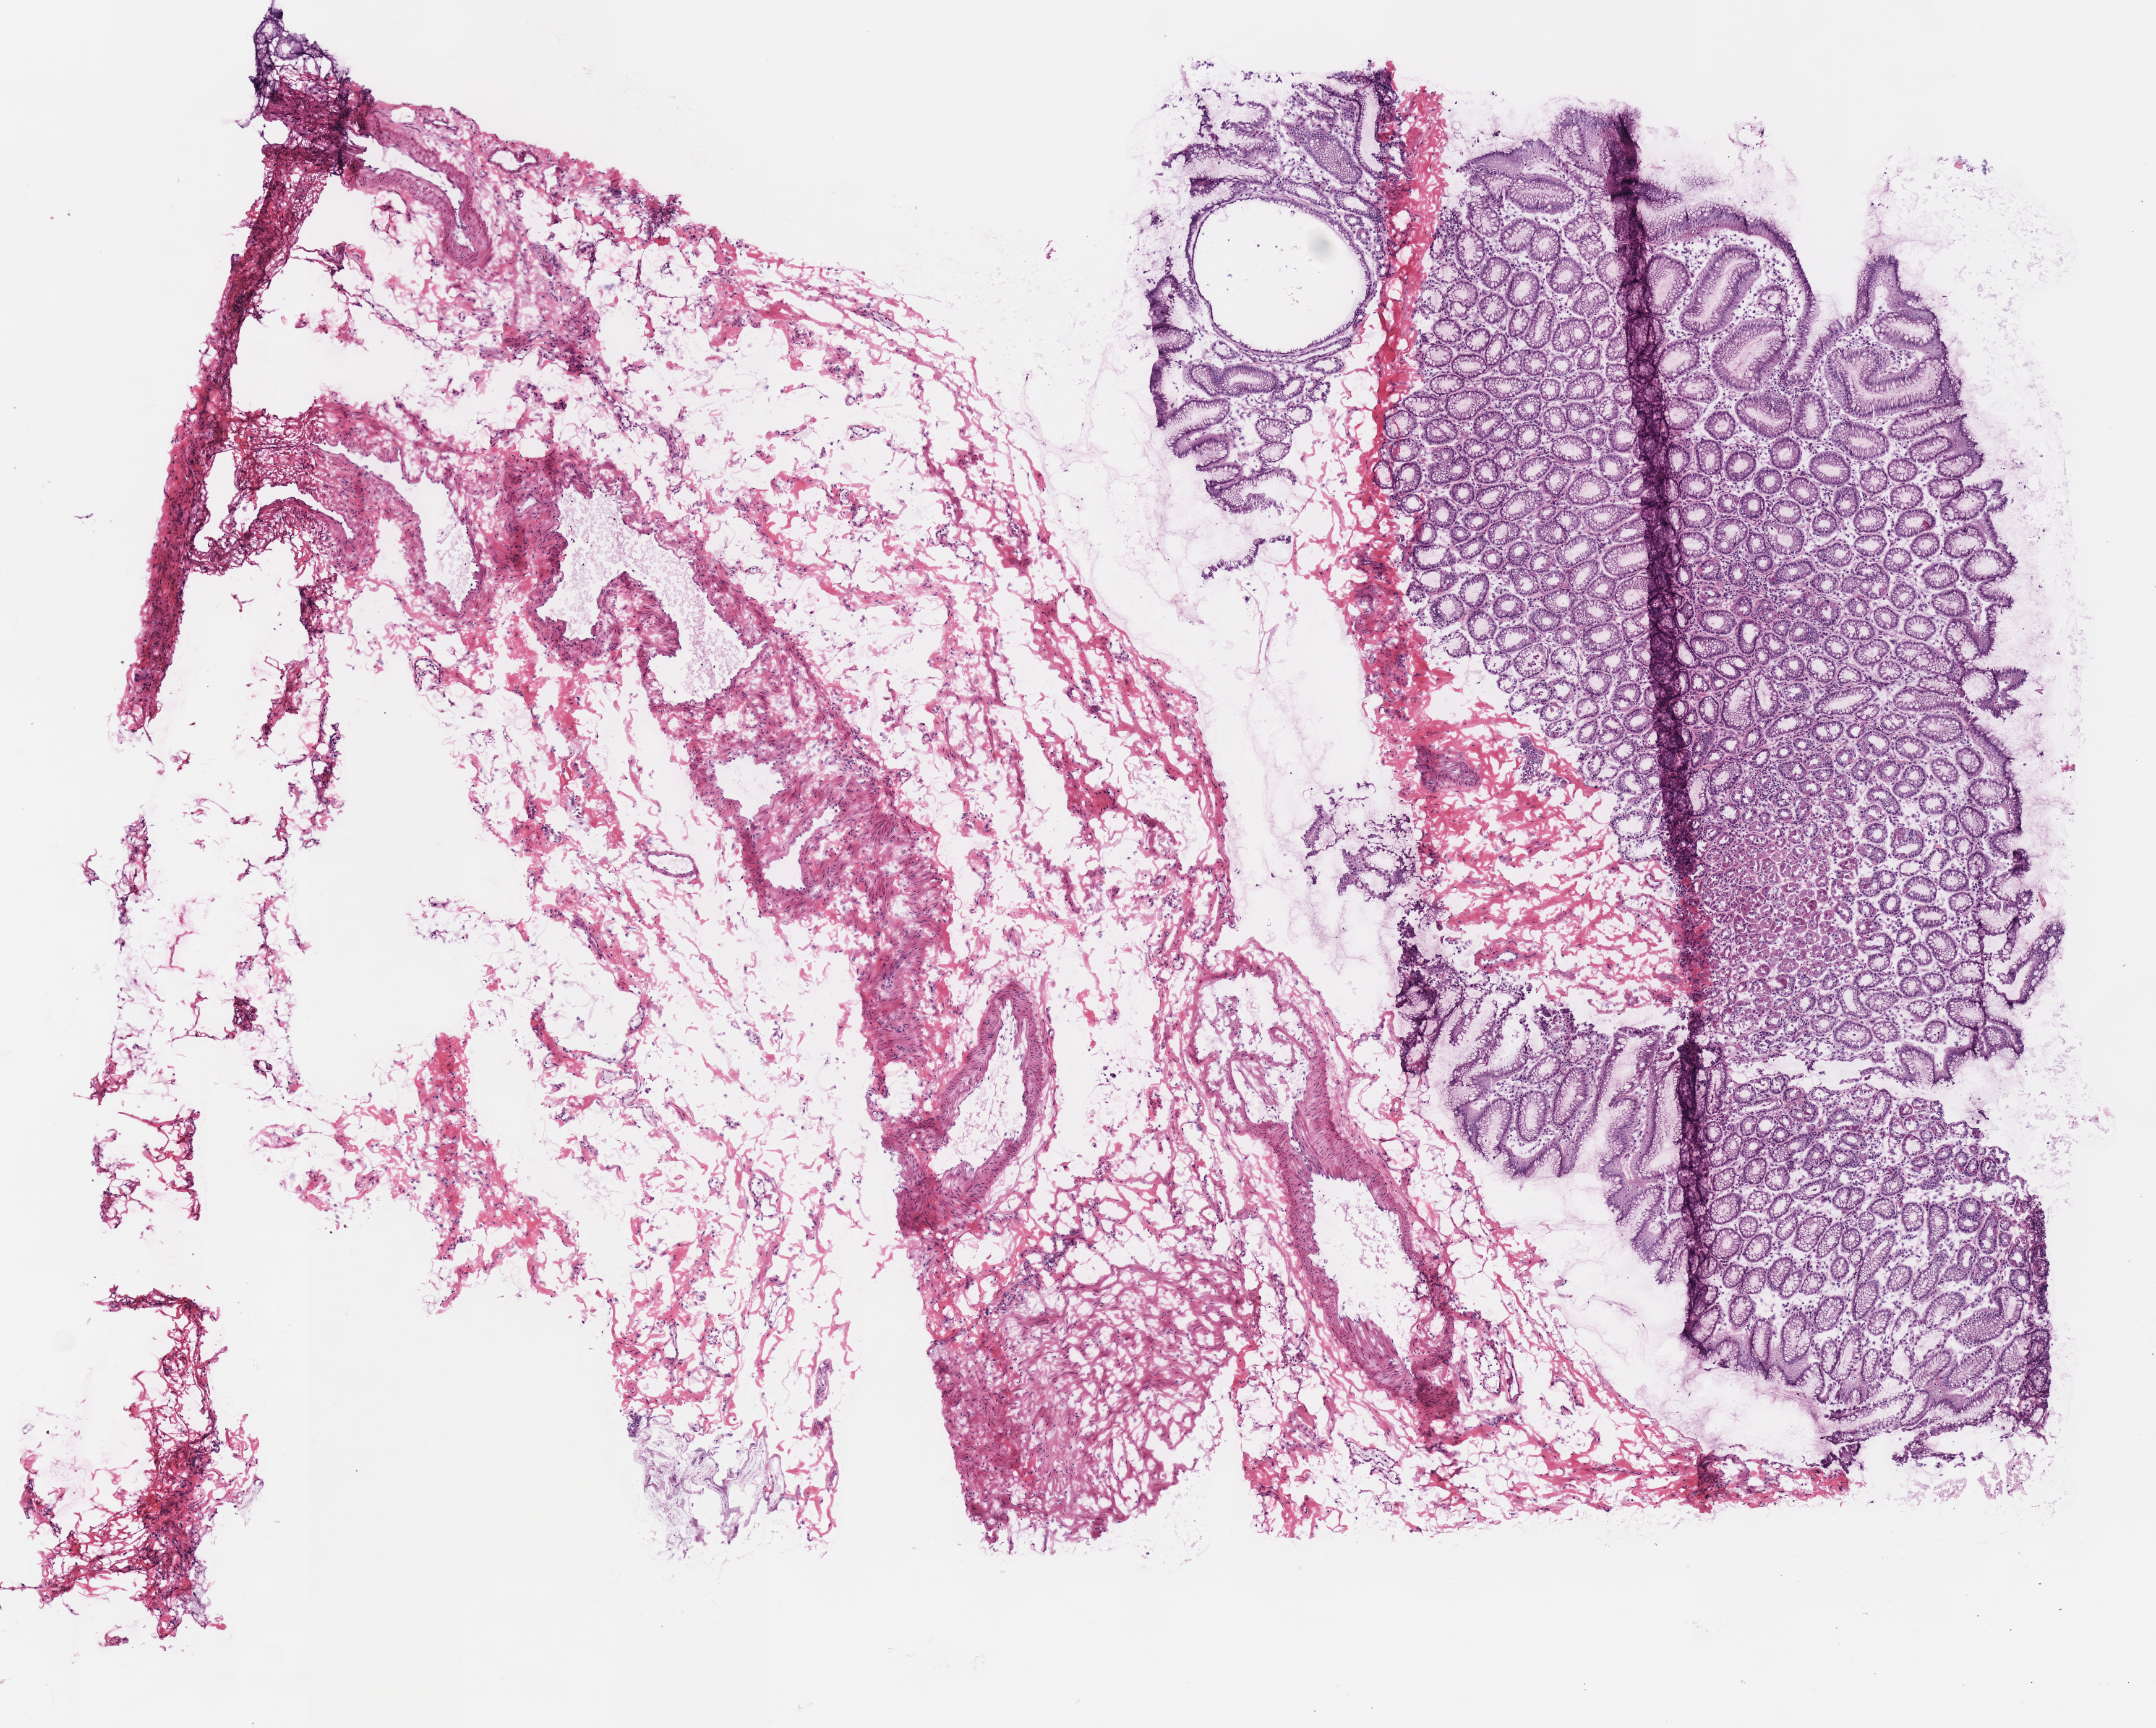
H&E whole-slide image — whole scanned area (about 6.9 x 5.5 mm, slide scanned at 40x) shown as a low-resolution overview. Frozen section from the top of the tissue portion. Sample: solid tissue normal (non-tumour tissue), stomach. Patient: female, age at initial diagnosis 82 years.
This section: solid tissue normal (non-tumour) sample from the same patient. Patient diagnosis: Tubular adenocarcinoma (gastric antrum).